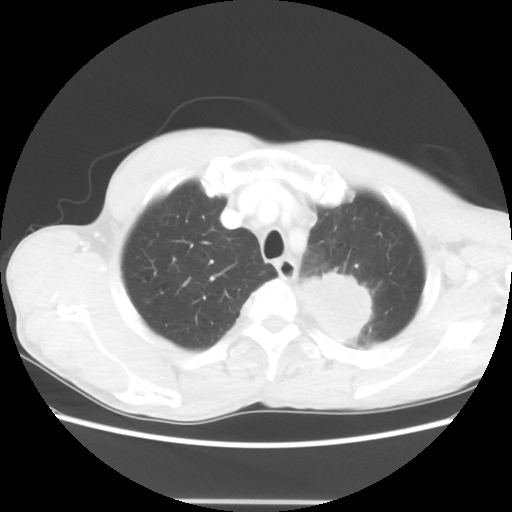
Chest CT, one axial slice. Position 54 of 62 along the scan axis. Reconstruction kernel STANDARD. 100 kVp. Lung window (W 1500 / L -600 HU). 5 mm slice thickness. 512 × 512 image matrix. Patient: male, 61 years. Case-level facts recorded for this patient, not image findings: clinical TNM (as recorded): T3 N1 M1.
Annotated regions visible in this slice (rectangle marked by the reading radiologist):
- lung tumour (recorded histology: adenocarcinoma): box from (x=299, y=265) to (x=389, y=344) px